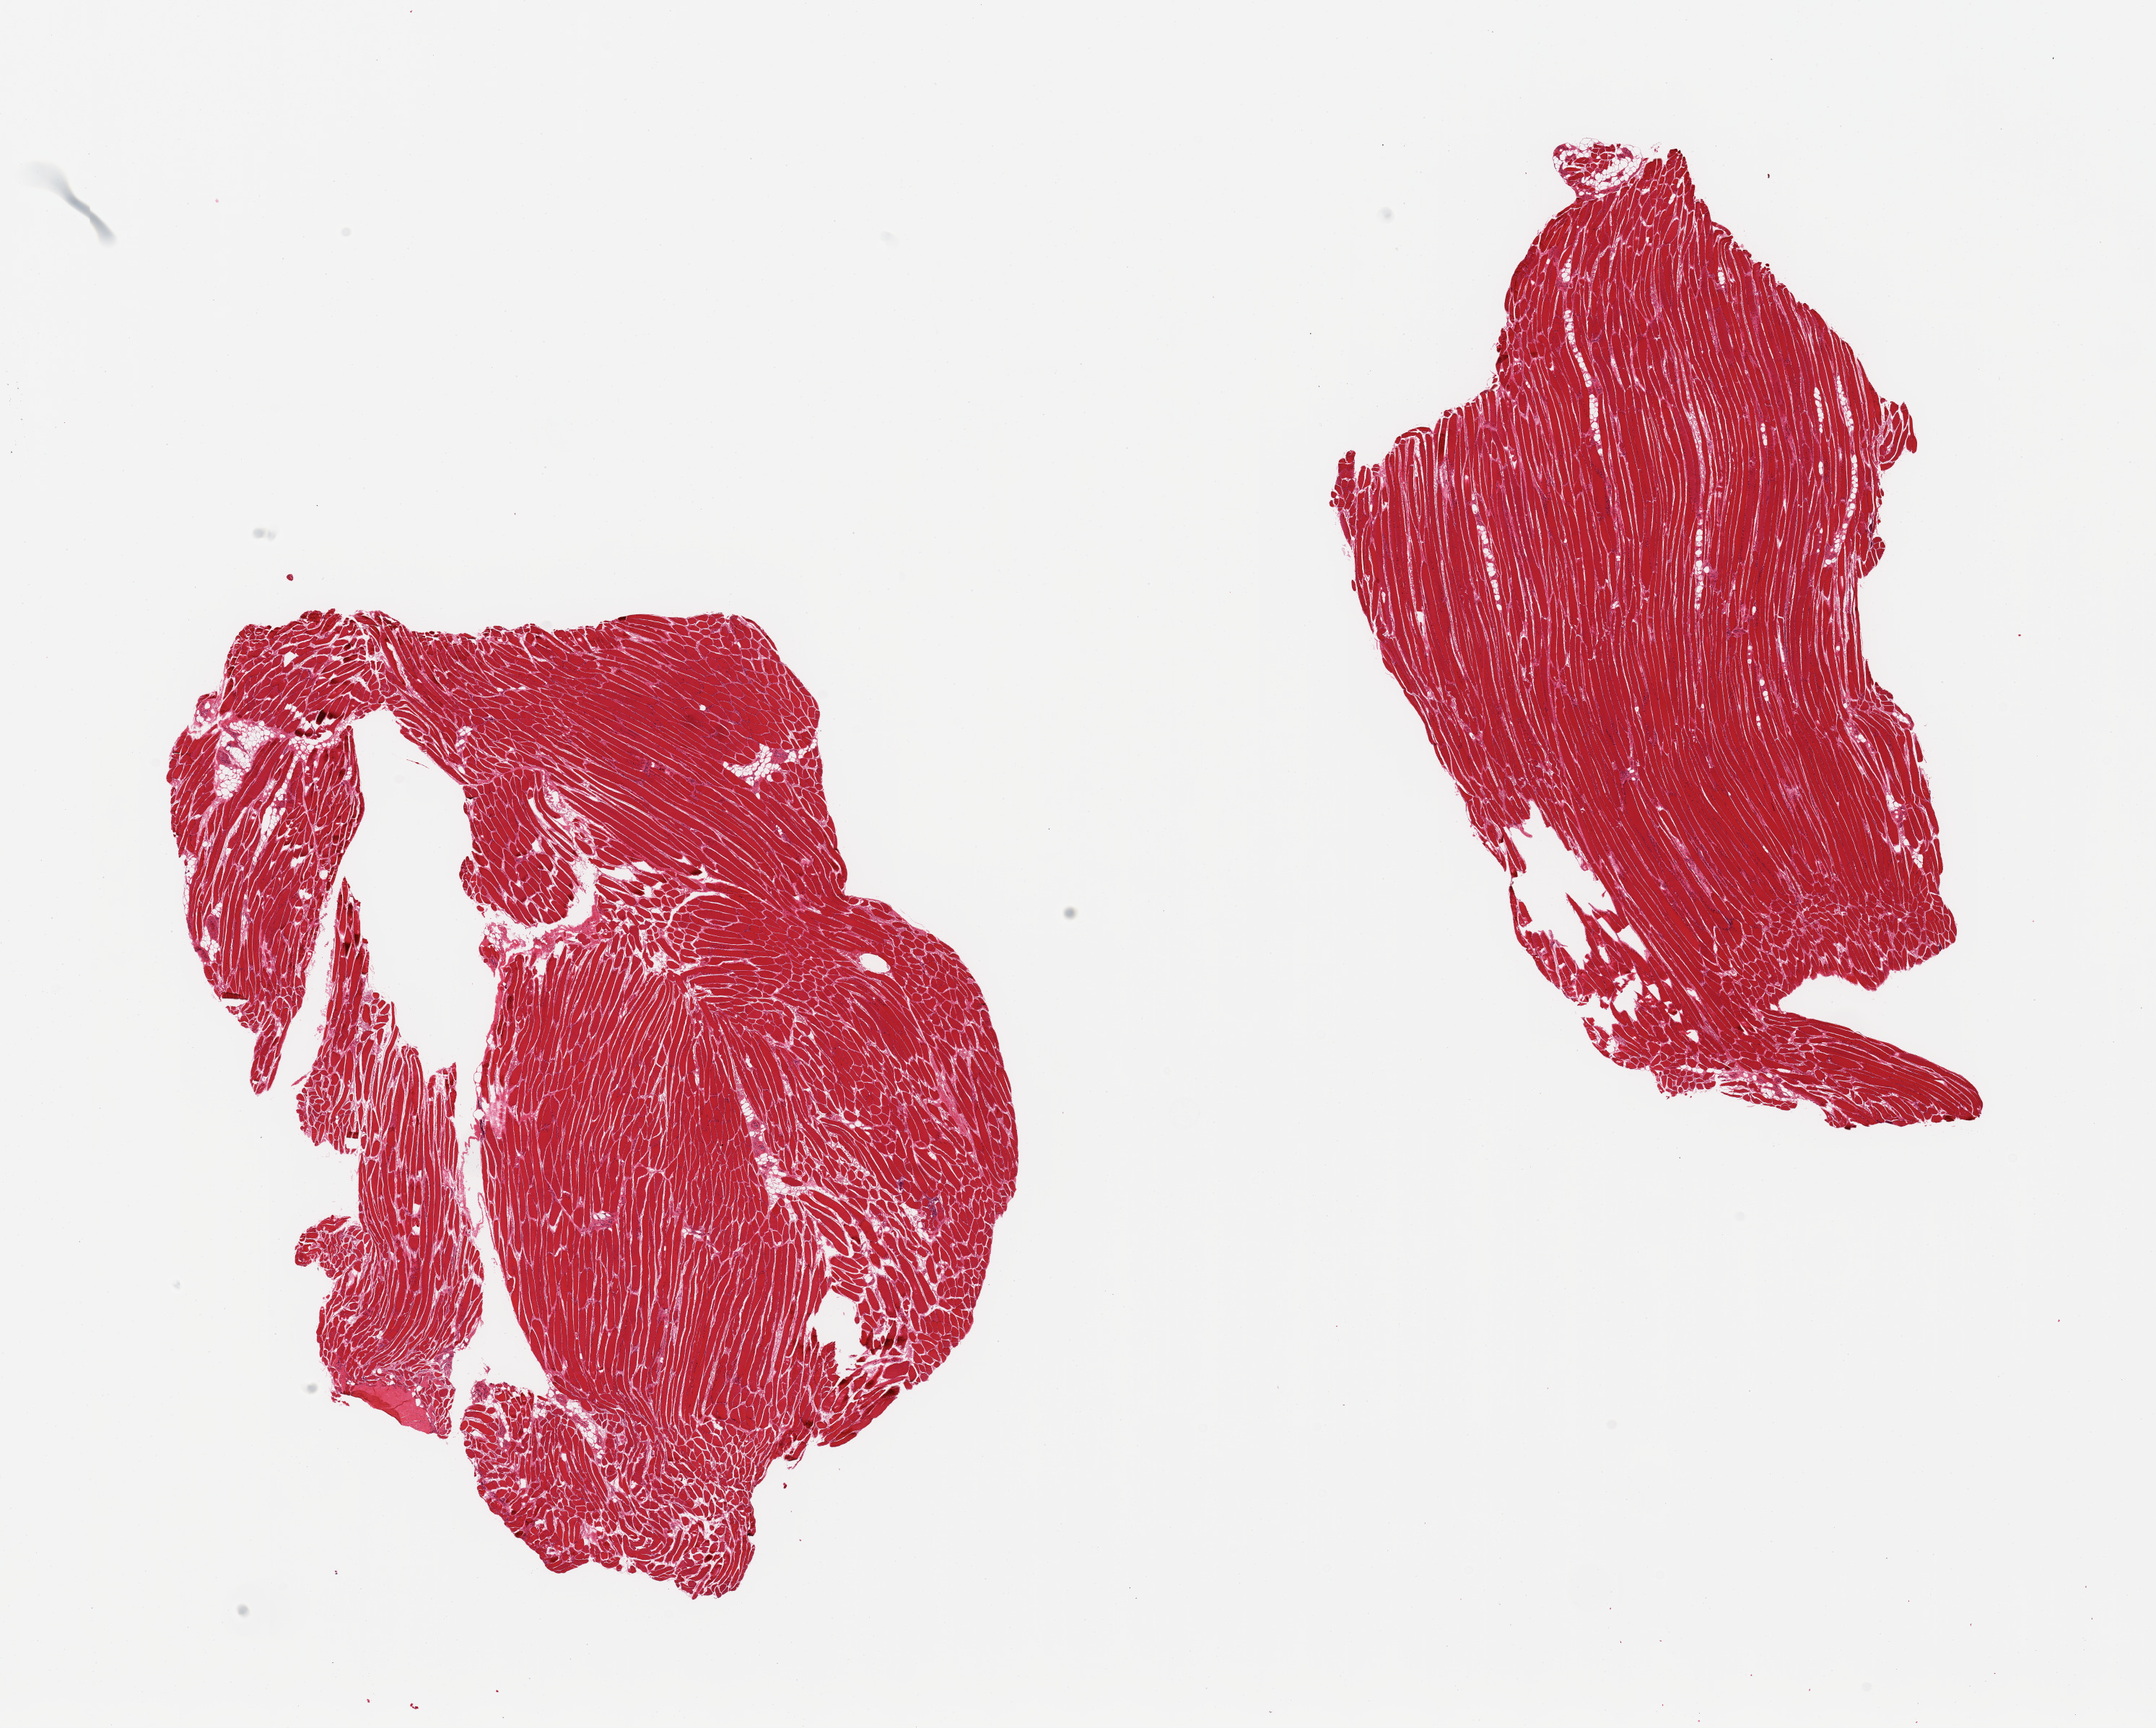
Digitized H&E-stained section — a low-resolution overview of the entire scanned area, about 23.6 x 18.9 mm (slide scanned at 20x). PAXgene-fixed paraffin-embedded (PFPE) section. Section of skeletal muscle (target tissue). Tissue donor sample. Donor sex: male.
* pathologist's review note for this sample: 2 pieces